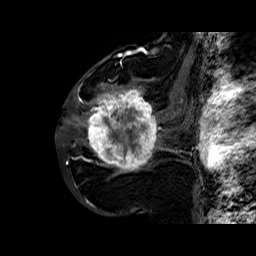
Breast MRI (dynamic contrast-enhanced), one sagittal slice. Slice 33 of 60 in the series (ordered by position). Dynamic contrast-enhanced series, time point 2 of 6 at this slice position (early post-contrast). 1.5 T. TE 6.4 ms, TR 32.8 ms. 4 mm slice thickness. 256 × 256 image matrix. Female patient. Case-level facts recorded for this patient, not image findings: setting: breast cancer imaged before/during neoadjuvant chemotherapy; receptor status: HR-positive, HER2-negative.
Annotated regions visible in this slice (semi-automatic segmentation, software-assisted and operator-edited):
- analysis volume of interest (the breast-tissue region the enhancement analysis was run in; not a lesion): box from (x=86, y=77) to (x=163, y=177) px
- tumour enhancement mask (voxels above the 100 % enhancement threshold inside the analysis volume of interest): (x=86, y=84)–(x=161, y=171)